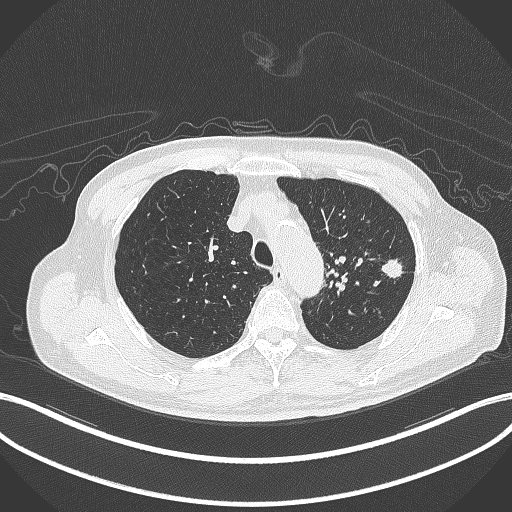
Chest CT, one axial slice; reconstruction kernel B70f; lung window (W 1500 / L -600 HU); 512 × 512 image matrix, field of view 400 × 400 mm. Male patient, age 77 years. Case-level facts recorded for this patient, not image findings: clinical TNM (as recorded): T3 N1 M0.
Structures marked on this image (bounding box drawn by a radiologist):
- lung tumour (recorded histology: adenocarcinoma): bounding box <380,254,405,278> (left, top, right, bottom; pixels)